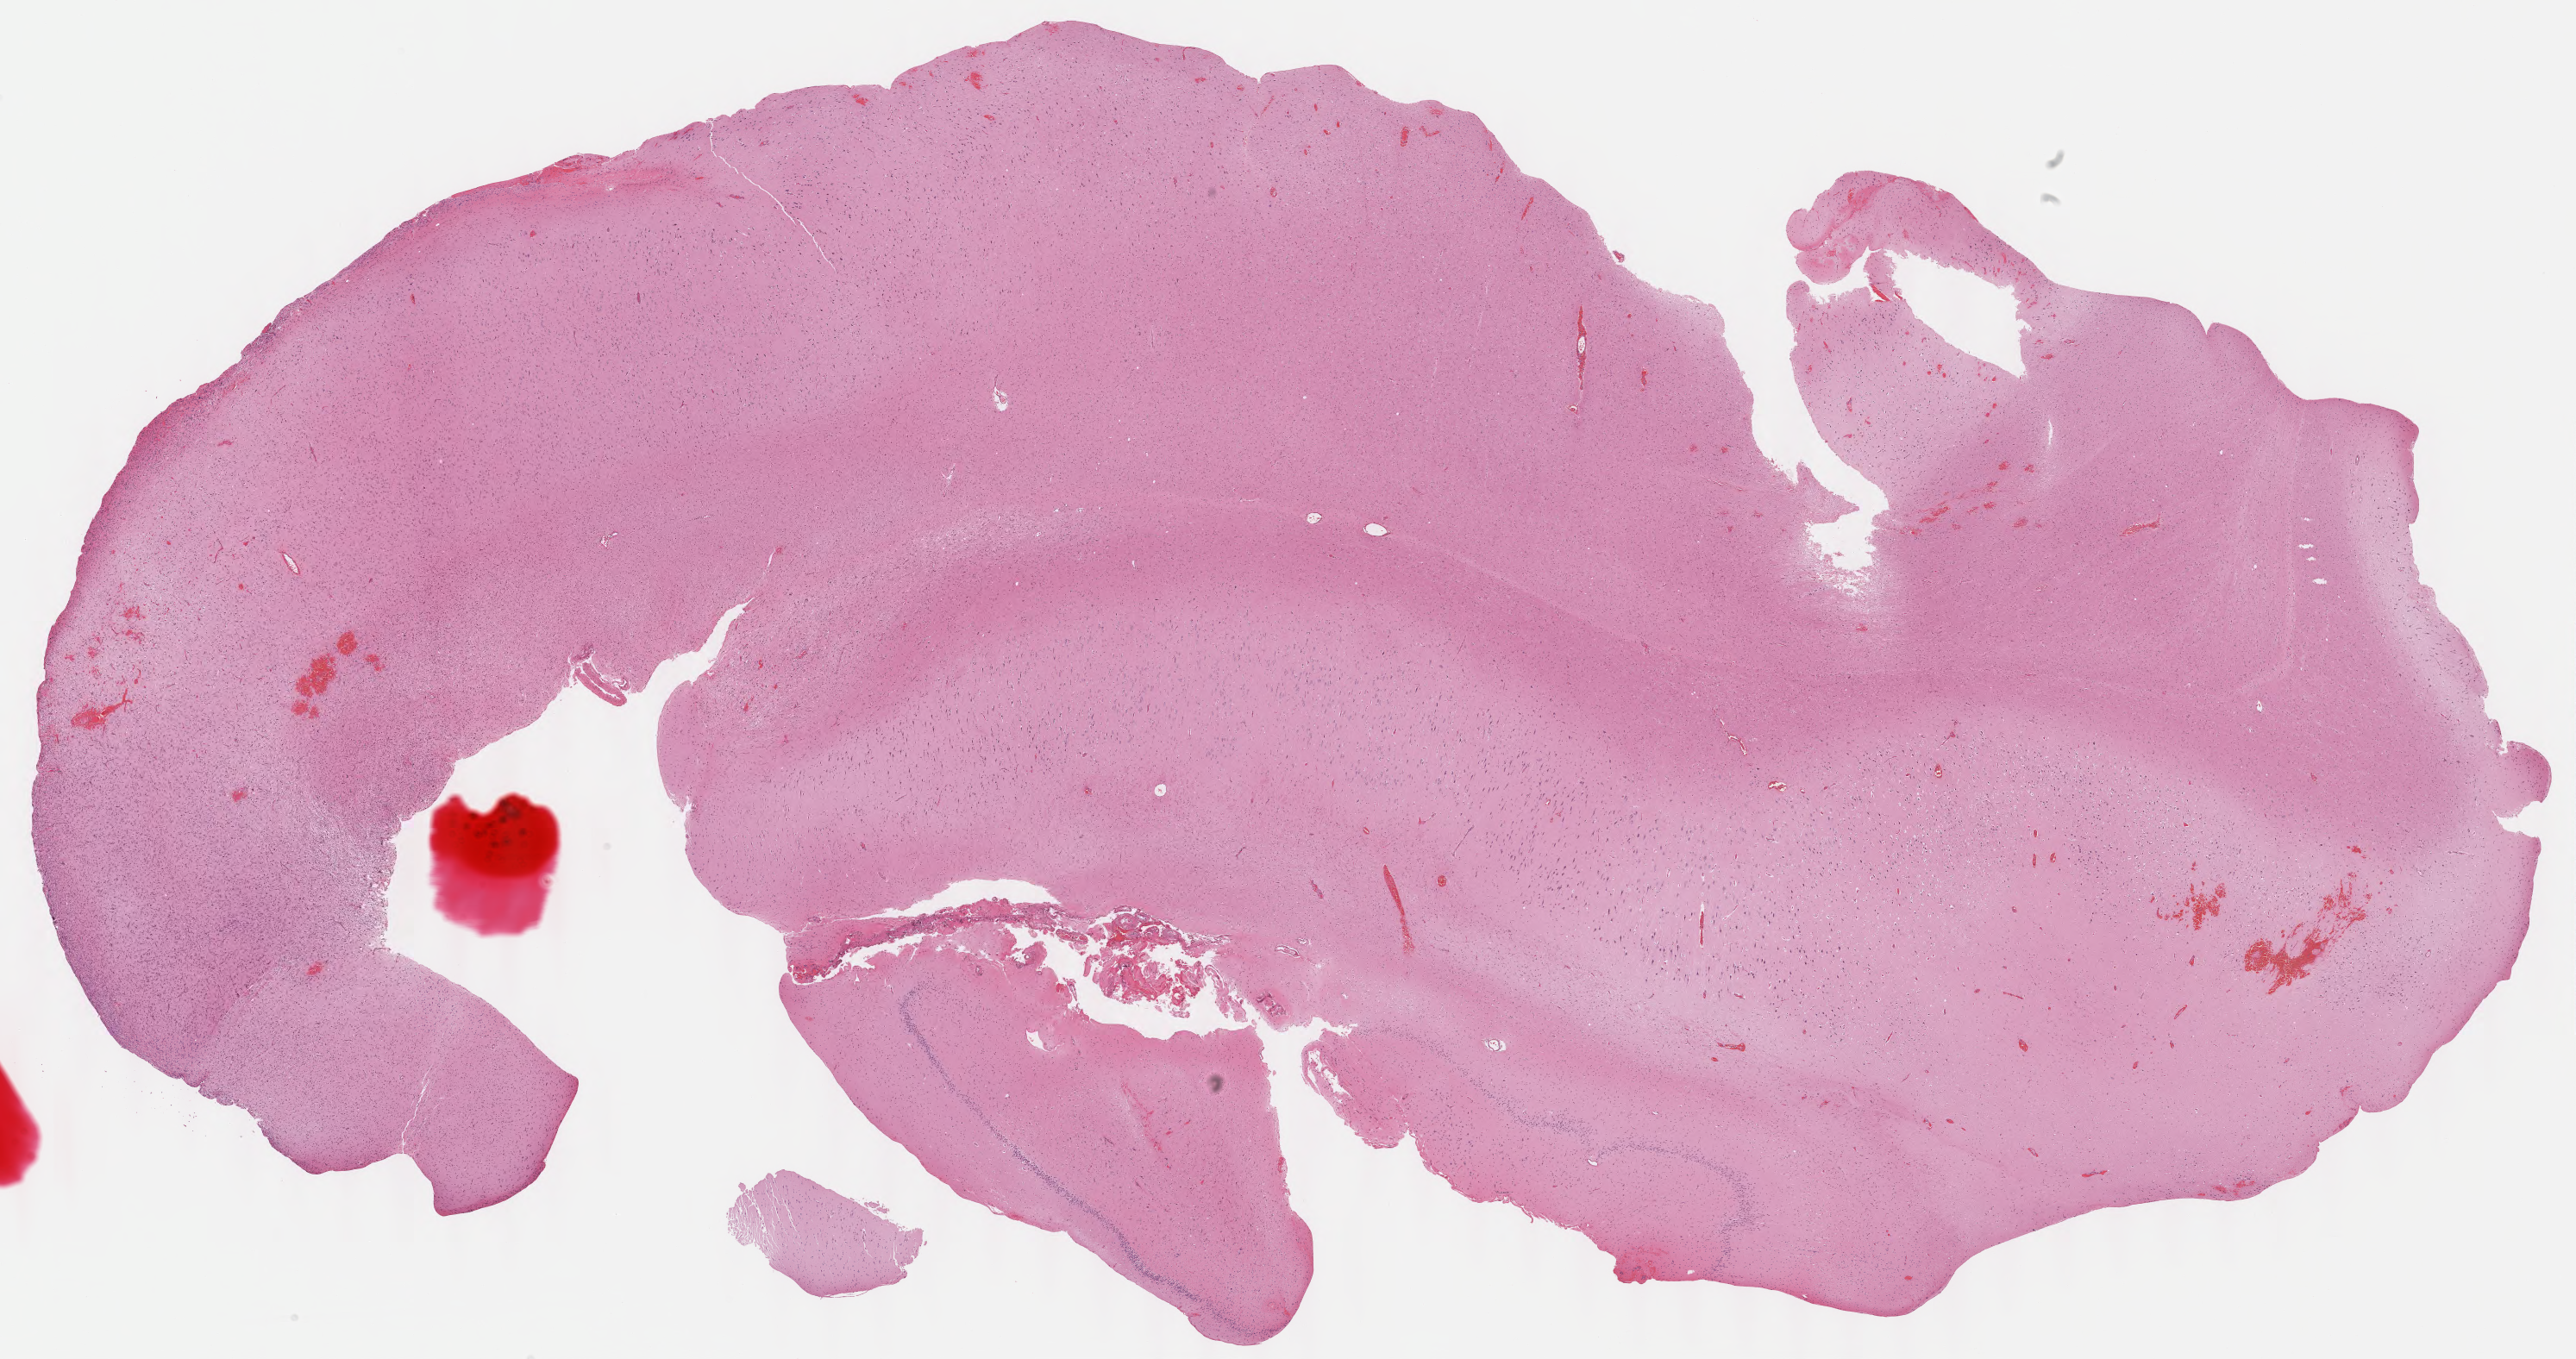
Digitized H&E tissue section (whole slide), shown as a low-resolution overview of the whole scanned area (about 23.6 x 12.5 mm, acquisition: 40x scan); formalin-fixed paraffin-embedded (FFPE) diagnostic section; sample: primary tumour, brain. Patient: female, age at initial diagnosis 25 years. Histologic grade: G2 (moderately differentiated).
Pathologic diagnosis: Astrocytoma, NOS (cerebrum). Laterality: right.